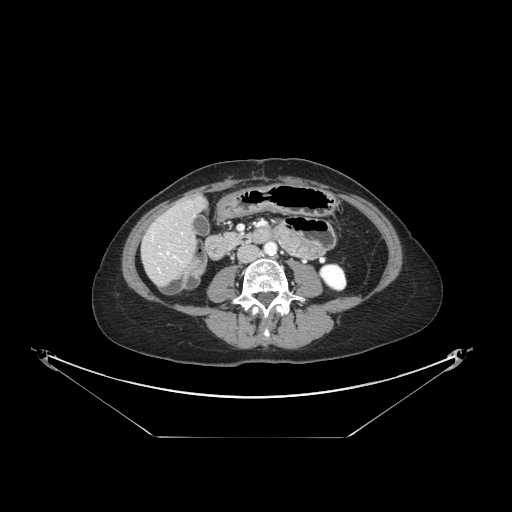
Contrast-enhanced abdominal CT, one axial slice; slice 37 of 148 in the series (ordered by position); reconstruction kernel STANDARD; 120 kVp; soft-tissue window (W 400 / L 40 HU); 2.5 mm slice thickness; 512 × 512 image matrix, field of view 500 × 500 mm. Female patient, age 73 years. Case-level facts recorded for this patient, not image findings: diagnosis: colorectal cancer liver metastases, imaged before liver resection; multiple liver metastases: no; largest metastasis: 1 cm; disease in both lobes: no.
Outlined on this slice (manually delineated by an expert):
- hepatic veins: bounding box (x1, y1, x2, y2) in pixels: (158, 253, 168, 269)
- liver: (143, 199, 204, 284)
- planned liver remnant (the part of the liver to remain after resection): (162, 199, 204, 240)